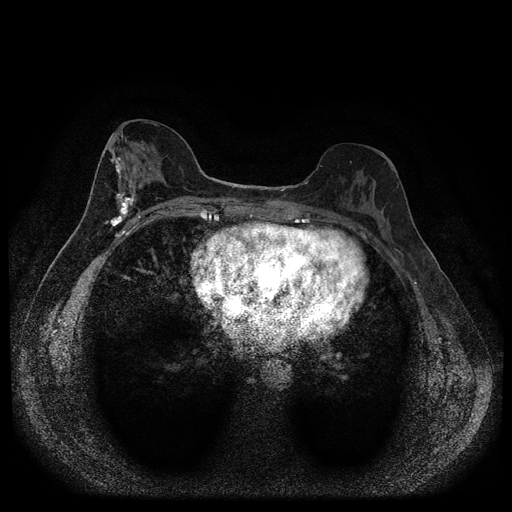
Breast MRI (dynamic contrast-enhanced, multi-phase), one axial slice. Position 45 of 116 along the scan axis. Dynamic contrast-enhanced series, time point 2 of 5 at this slice position (early post-contrast). 1.5 T. TE 2.7 ms, TR 5.4 ms. 2 mm slice thickness. 512 × 512 image matrix. Patient: female, 49 years.
Annotated regions visible in this slice (semi-automatic segmentation, software-assisted and operator-edited):
- breast lesion (labelled 'tumour' in the annotation; benign lesions carry a separate 'benign' label): bounding box <103,155,138,232> (left, top, right, bottom; pixels)